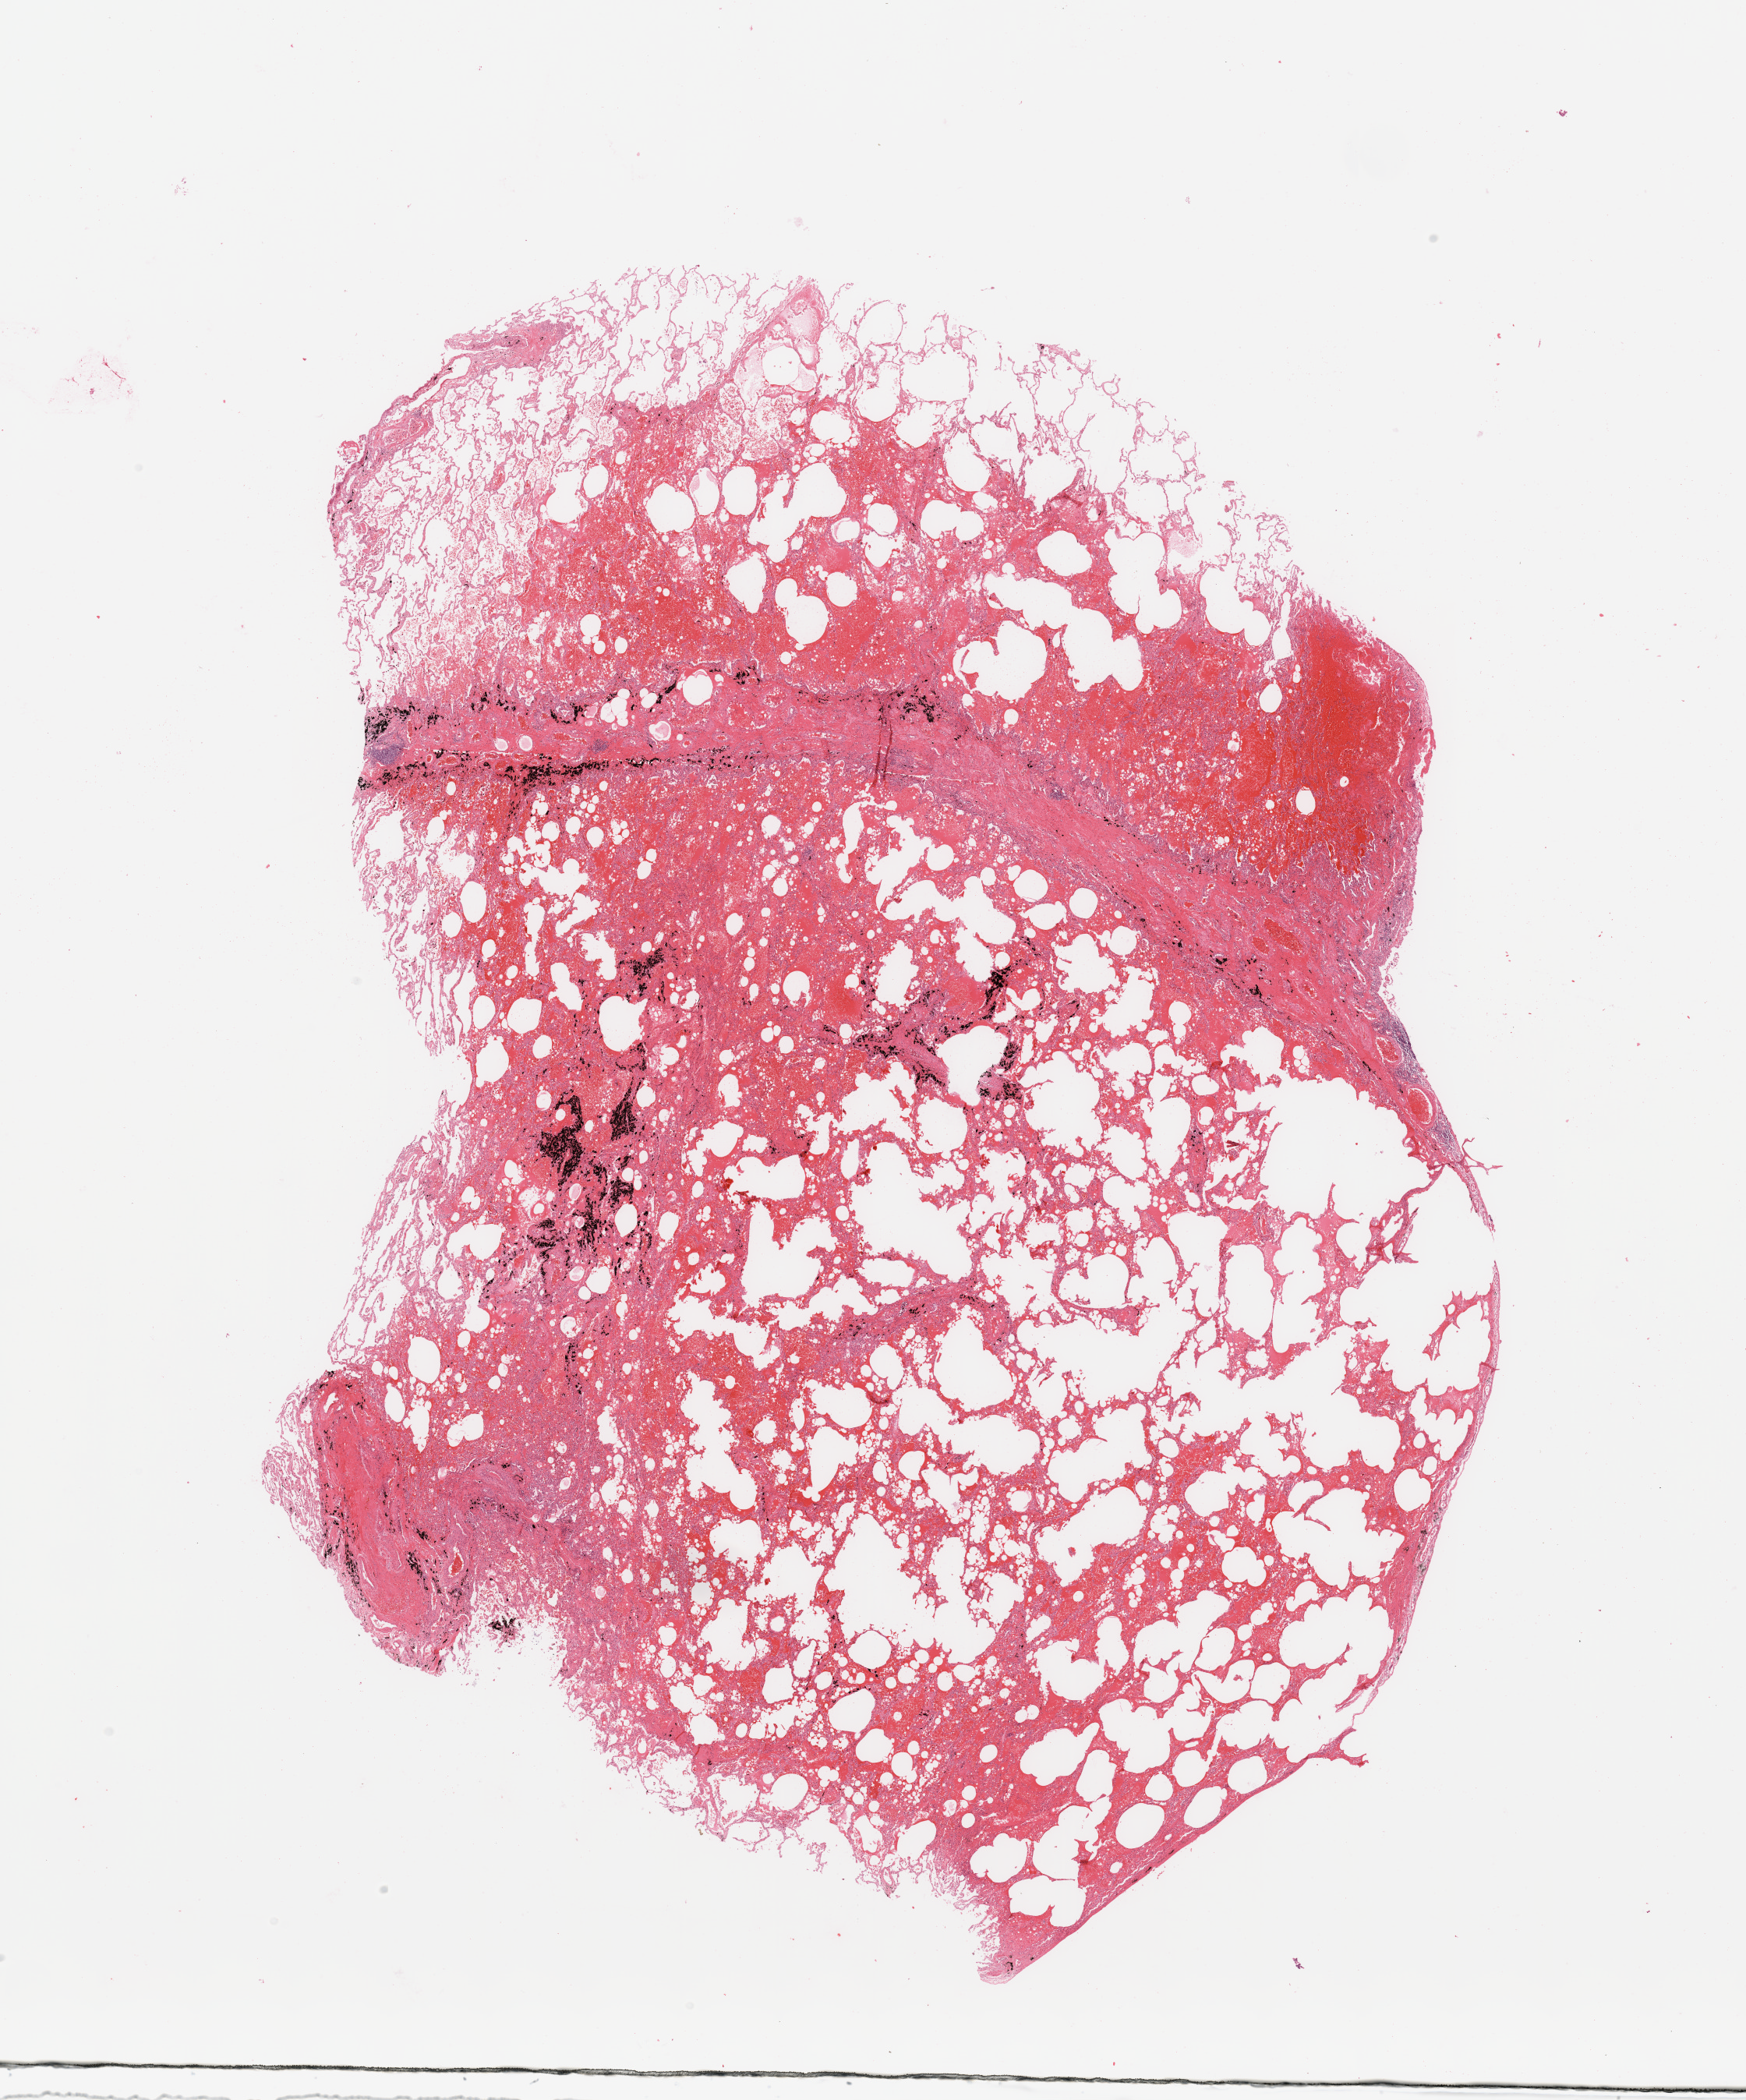
Hematoxylin and eosin (H&E) stained whole-slide image — shown as a low-resolution overview of the whole scanned area (about 17.7 x 21.3 mm, acquisition: 20x scan). Normal (non-tumour) tissue sample, lung. 59-year-old male patient.
• this section: normal (non-tumour) tissue from the same patient
• patient diagnosis: Adenocarcinoma, NOS